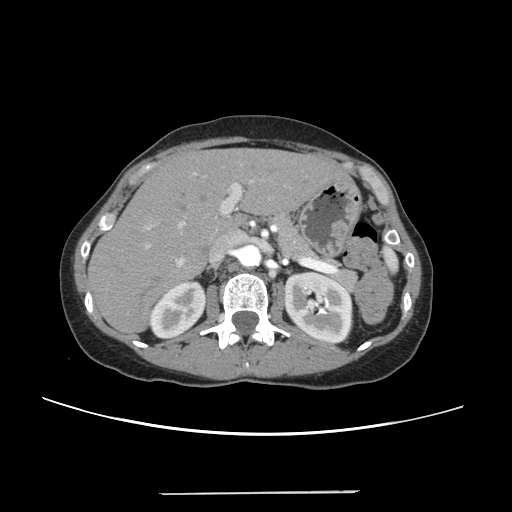
Contrast-enhanced abdominal CT, one axial slice; slice 152 of 240 in the series (ordered by position); 120 kVp; soft-tissue window (W 400 / L 40 HU); 1.25 mm slice thickness; 512 × 512 image matrix, field of view 371 × 371 mm. Female patient, age 60 years. From the clinical record (not read from this slice): diagnosis: colorectal cancer liver metastases, imaged before liver resection; multiple liver metastases: no; largest metastasis: 1.5 cm; disease in both lobes: no.
Outlined on this slice (manually delineated by an expert):
- liver: box from (x=90, y=150) to (x=344, y=331) px
- planned liver remnant (the part of the liver to remain after resection): (x=90, y=150)–(x=343, y=331)
- portal vein (with intrahepatic branches): (x=144, y=171)–(x=255, y=266)